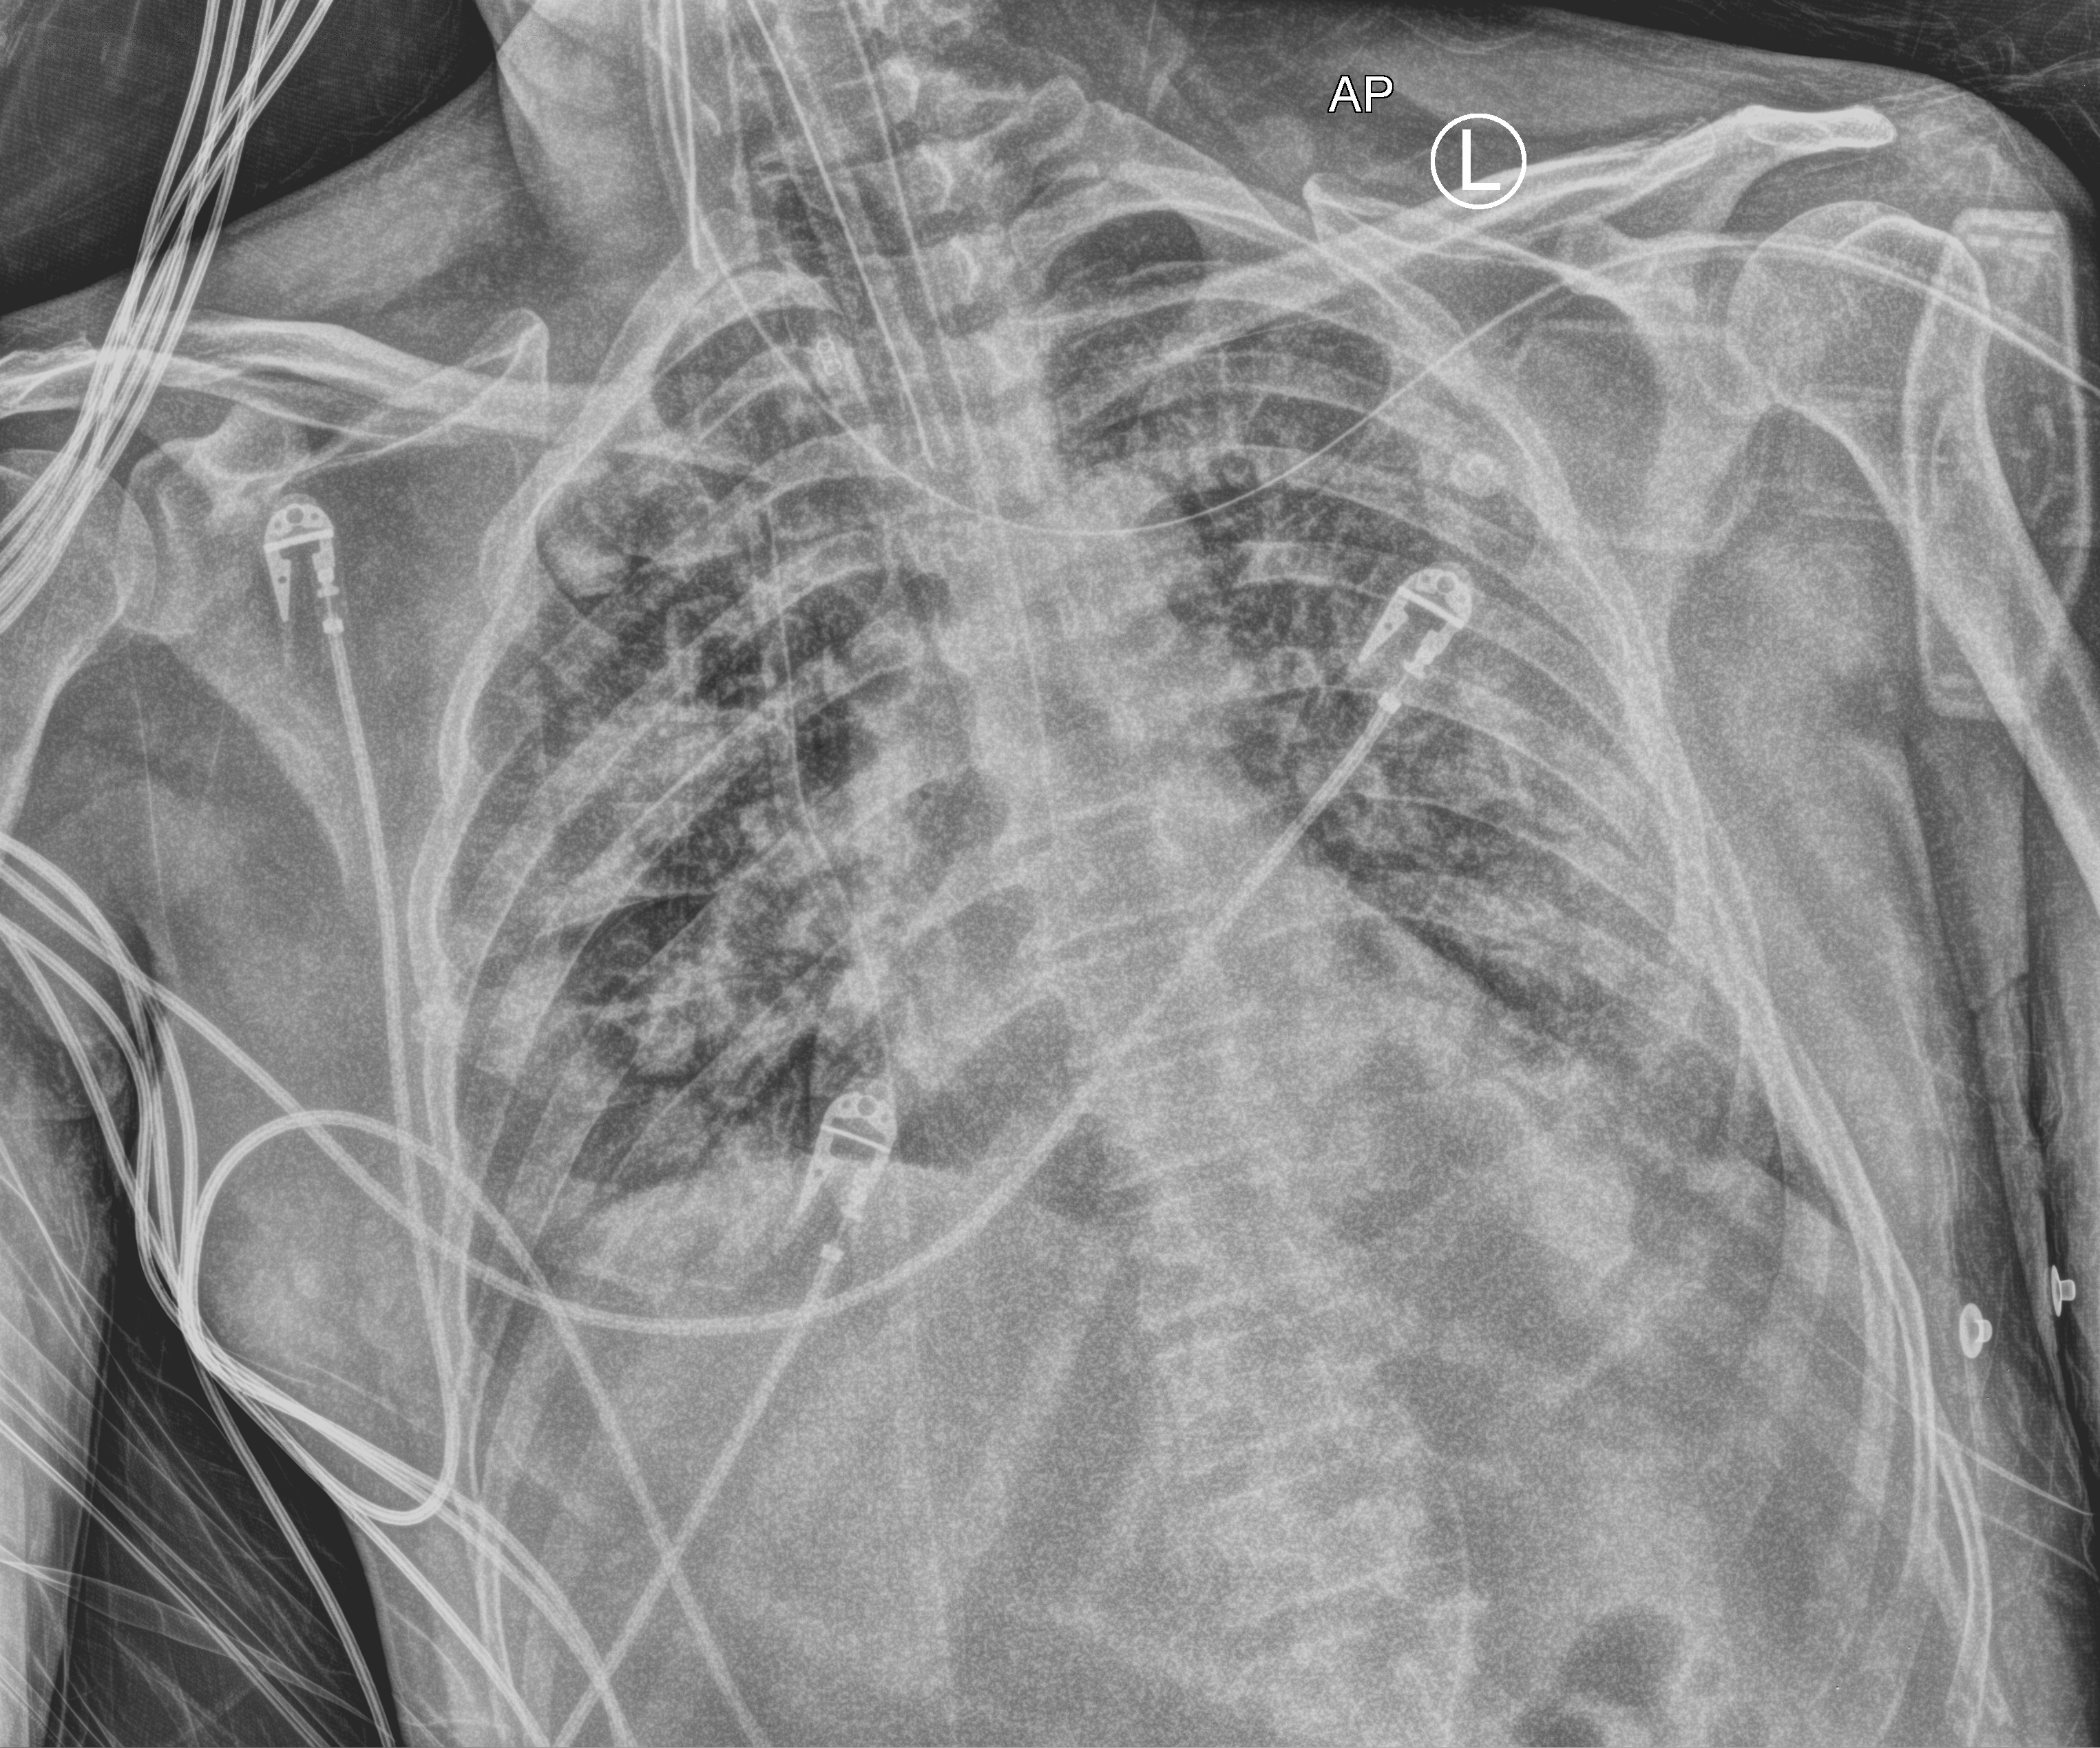
Chest X-ray (portable); anteroposterior (AP) projection. Patient hospitalised with COVID-19; male, aged 18–59 years.
Hospital-stay facts (about this admission, not read from this image; timing relative to this image not recorded): mechanically ventilated during this hospital stay: yes; chronic kidney disease (admission record): no.